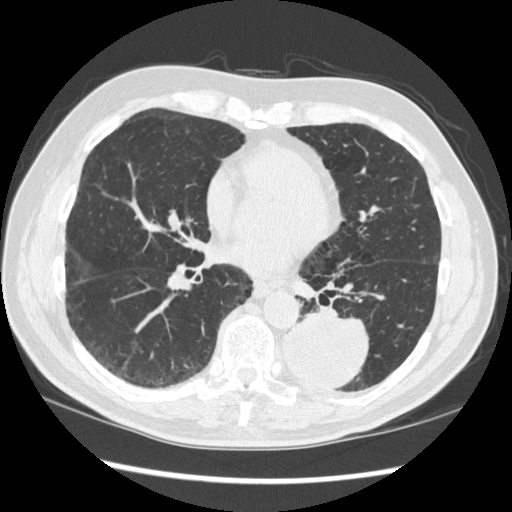
Axial slice from a low-dose chest CT screening exam, baseline screening round, lung window (W 1500 / L -600 HU), 1.25 mm slice thickness. Male, age 72 years at enrolment. Current smoker at enrolment.
Lesion marked by an expert reader, box from (x=268, y=302) to (x=372, y=393) px. The screening reader recorded 2 non-calcified nodules or masses ≥4 mm on this exam (left lower lobe, right middle lobe); which of them this box marks is not recorded. Lung cancer was diagnosed 37 days after this screen: squamous cell carcinoma, NOS, left lower lobe, stage IIIA (AJCC 6th edition), 60 mm at pathology.